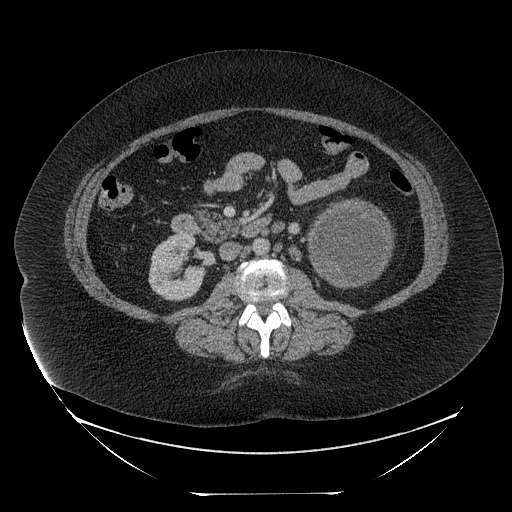
Contrast-enhanced abdominal CT, one axial slice. Reconstruction kernel STANDARD. 120 kVp. Intravenous contrast given. Soft-tissue window (W 400 / L 40 HU). 512 × 512 image matrix, field of view 500 × 500 mm. Female patient, age 53 years. Case-level facts recorded for this patient, not image findings: diagnosis: adrenocortical carcinoma; tumour side: left adrenal.
Annotated regions visible in this slice (semi-automatic segmentation, software-assisted and operator-edited):
- mass: bounding box (x1, y1, x2, y2) in pixels: (312, 202, 390, 284)